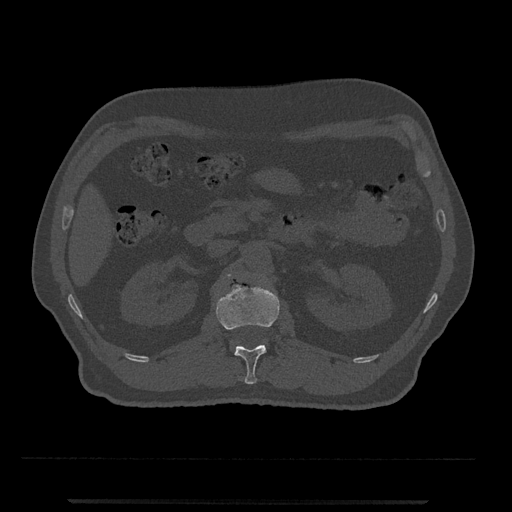
CT including the spine, one axial slice; slice 316 of 797 in the series (ordered by position); 120 kVp; bone window (W 1800 / L 400 HU); 0.5 mm slice thickness; 512 × 512 image matrix, field of view 419 × 419 mm. Patient: male, 63 years. Case-level facts recorded for this patient, not image findings: primary cancer: prostate.
Annotated regions visible in this slice (semi-automatic segmentation, software-assisted and operator-edited):
- L1 vertebra: bounding box (x1, y1, x2, y2) in pixels: (216, 285, 280, 384)
- L2 vertebra: (227, 274, 231, 278)